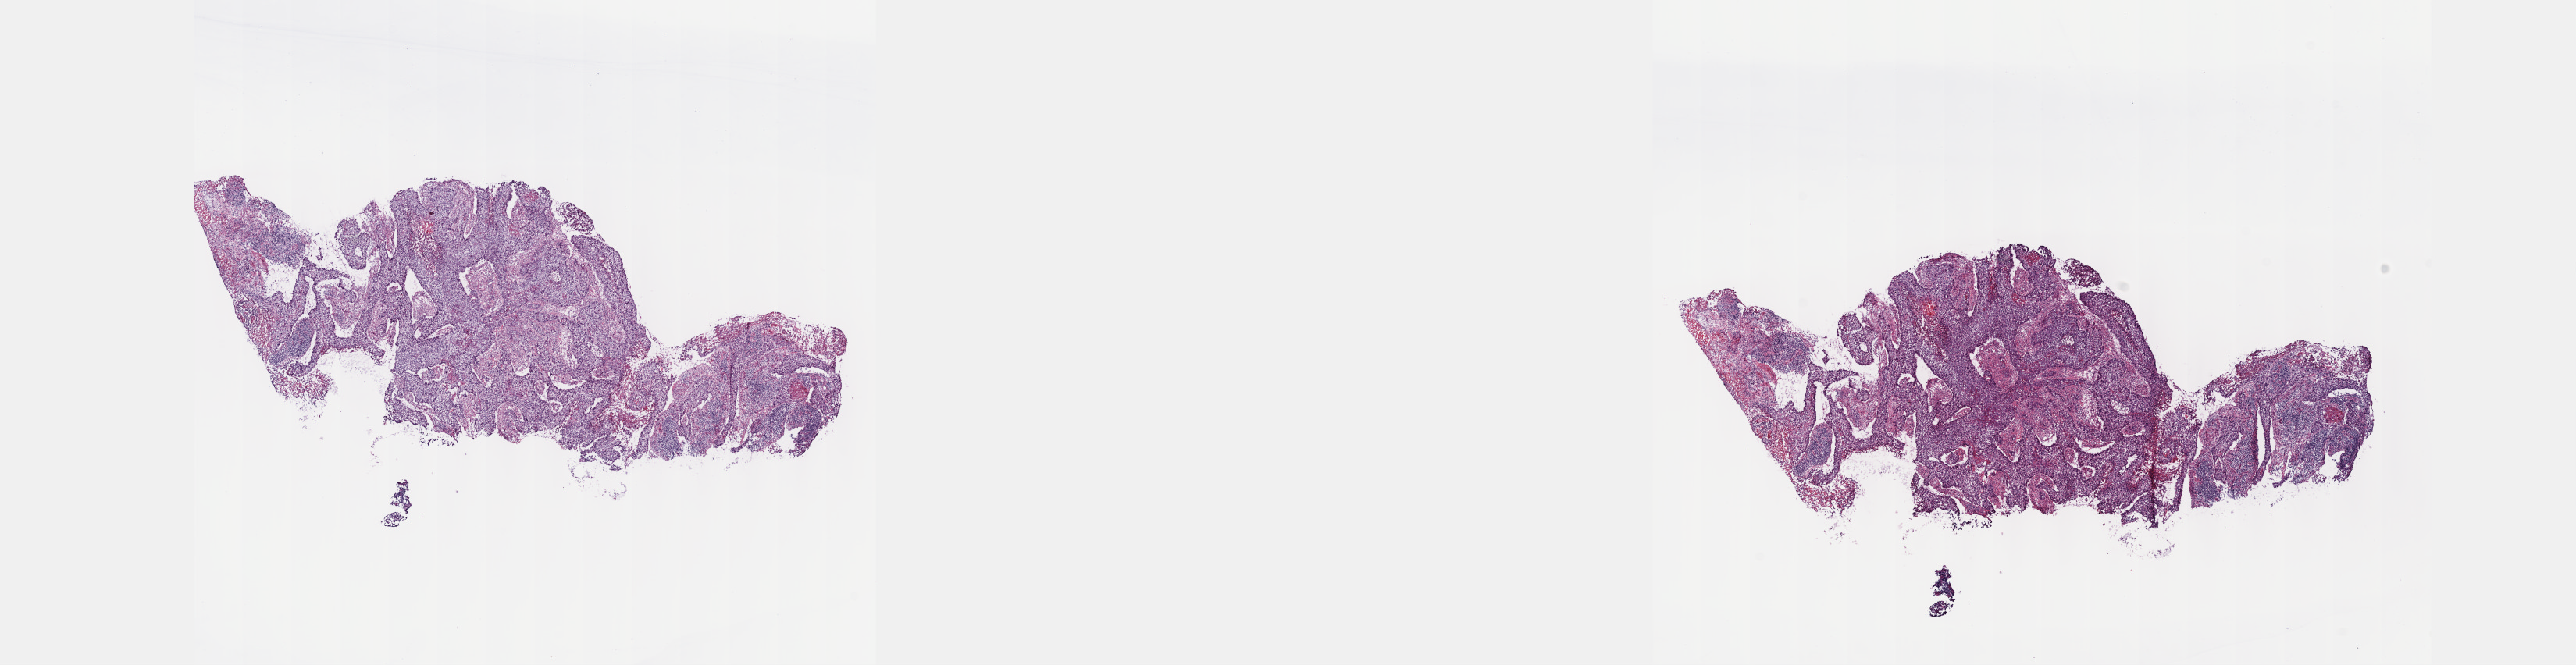
H&E whole-slide image, shown as a low-resolution overview of the whole scanned area (about 26.7 x 6.9 mm, slide scanned at 40x). Frozen section. Primary tumour sample from the cervix. Female patient; age at initial diagnosis 42 years. Histologic grade: G3 (poorly differentiated). Pathologist review of this section (percent, as recorded): tumour cells 70%, tumour nuclei 70%, normal cells 0%, stromal cells 20%, necrosis 10%. Infiltration values recorded for this section: lymphocyte infiltration 40%, monocyte infiltration 20%, neutrophil infiltration 20%.
FIGO stage: IIIA. Pathologic diagnosis: Squamous cell carcinoma, NOS (cervix uteri).